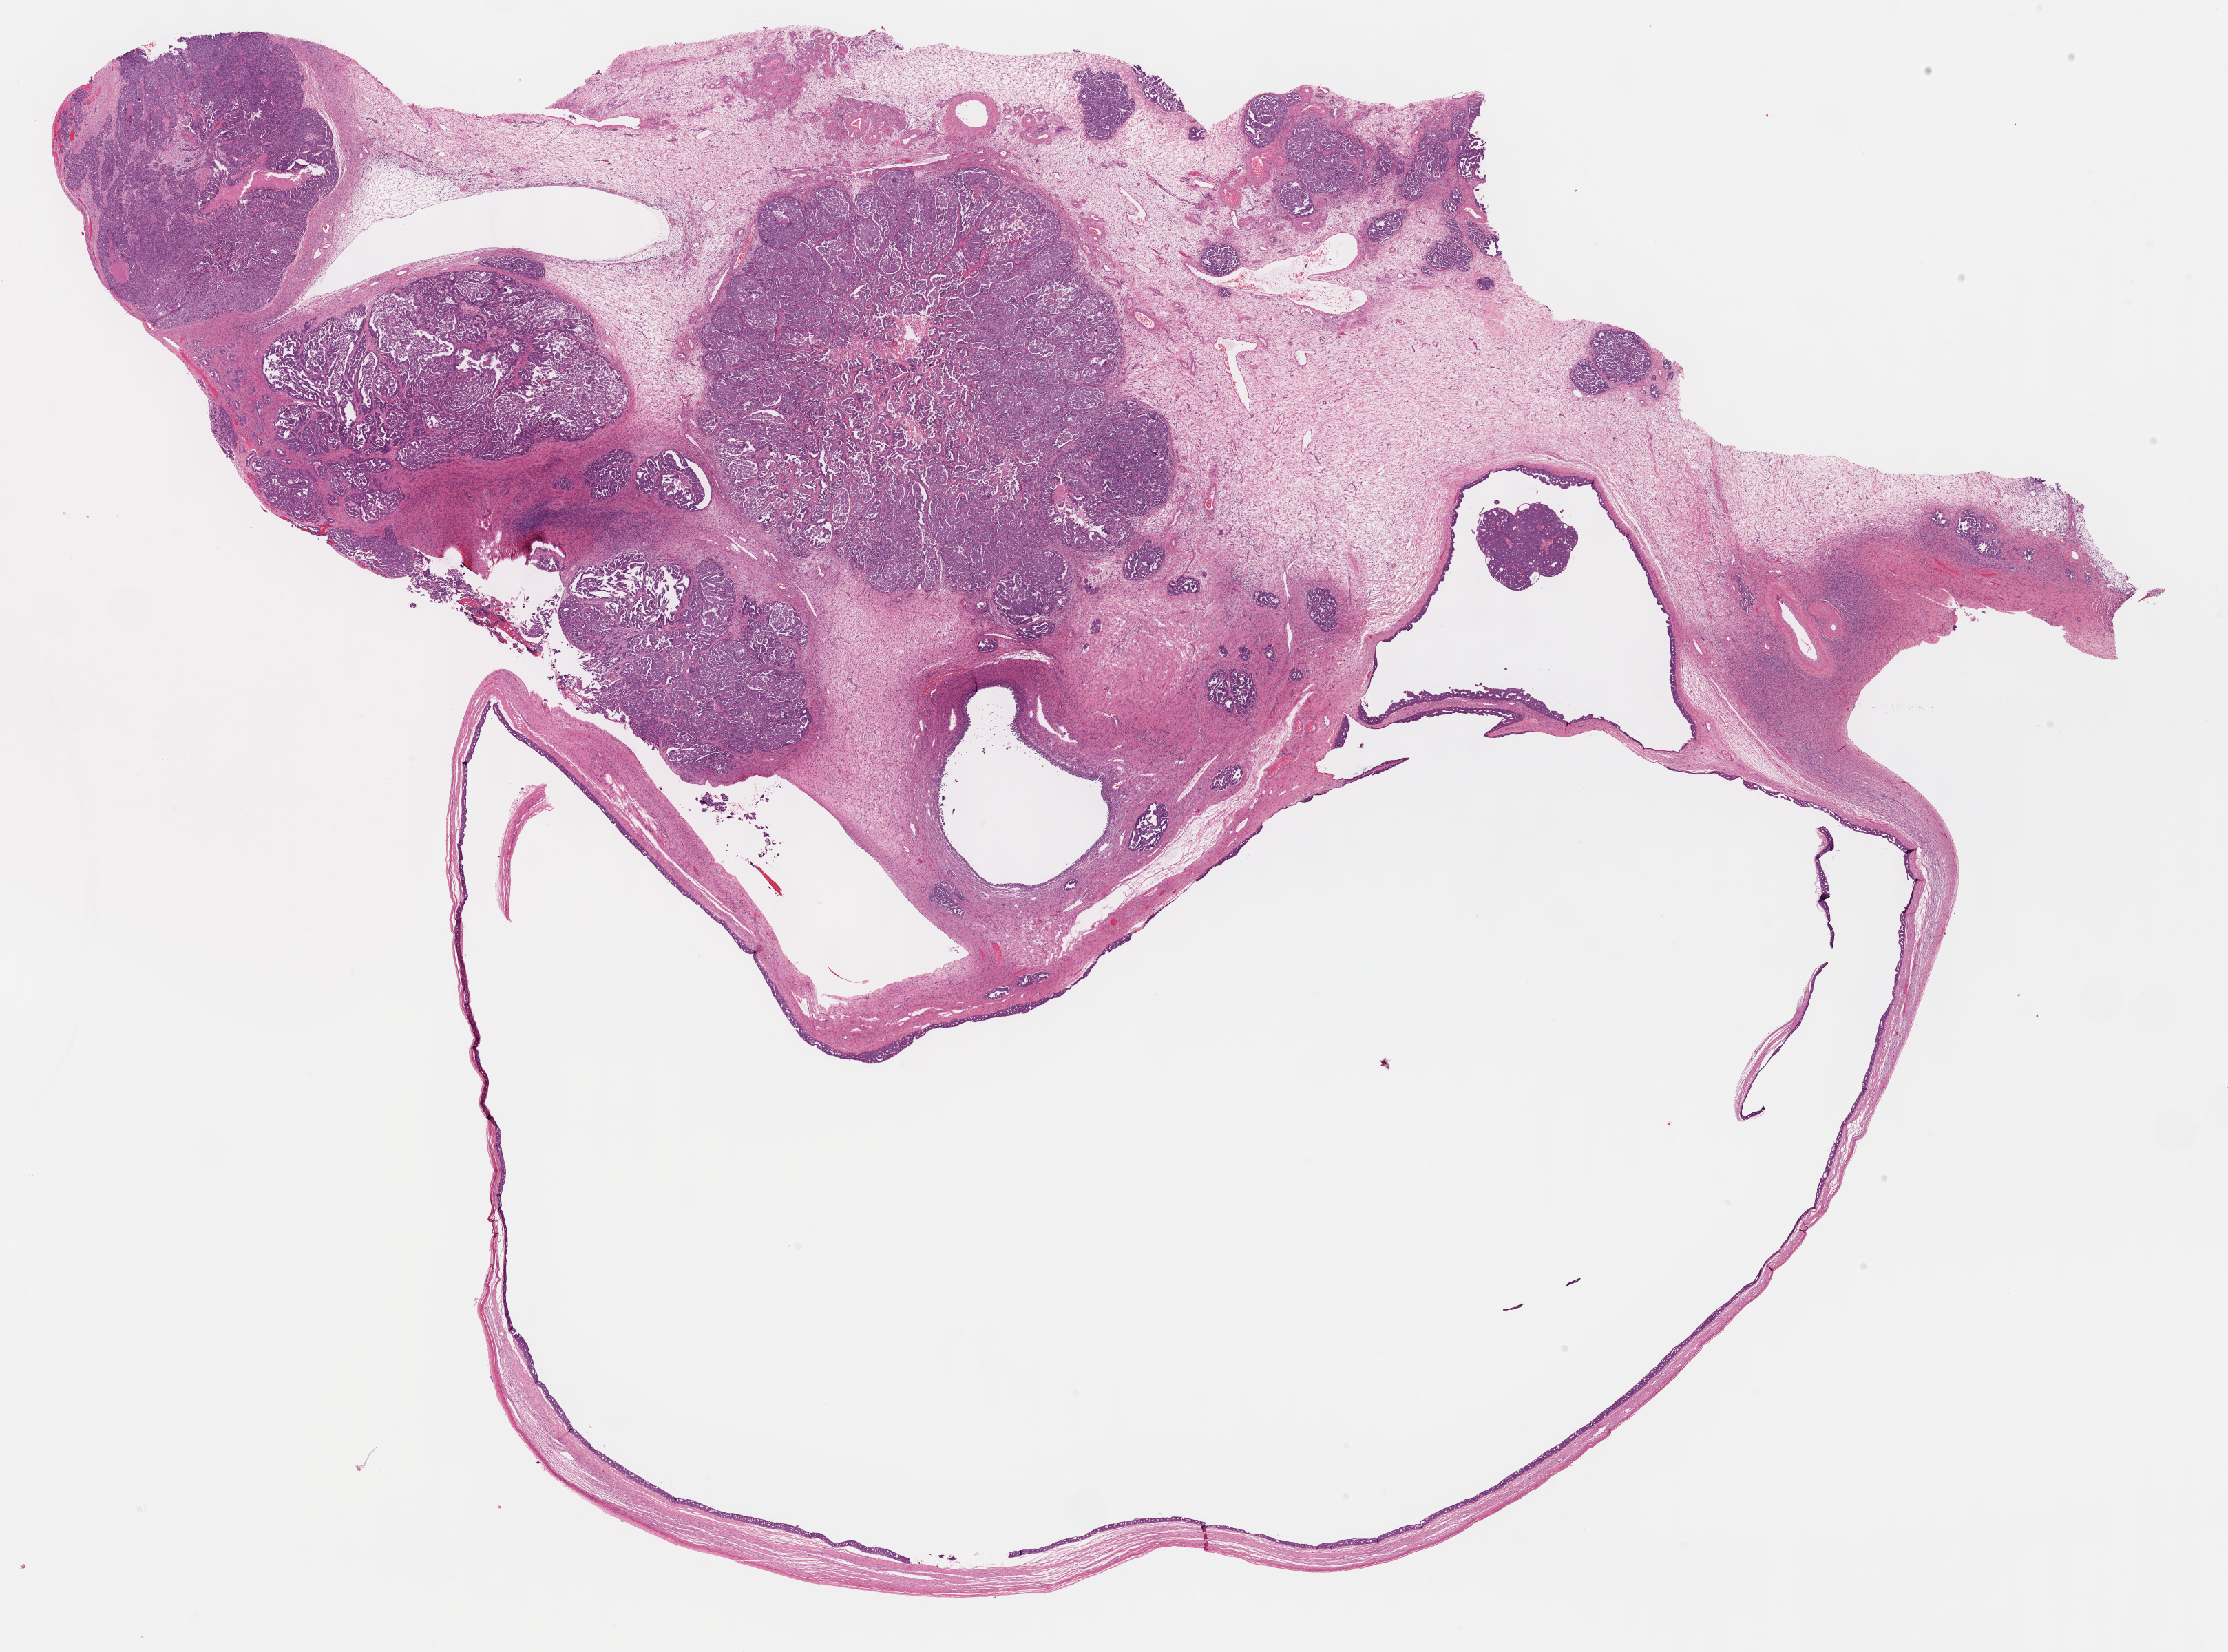
Digitized Hematoxylin and eosin (H&E) stained tissue section (whole slide) — low-resolution overview of the scanned area, about 26.2 x 19.4 mm (acquisition: 40x scan); FFPE section; primary tumour sample from the ovary. Patient: female, age at initial diagnosis 48 years. Histologic grade: G3 (poorly differentiated).
* laterality: left
* diagnosis: Serous cystadenocarcinoma, NOS
* FIGO stage: IV